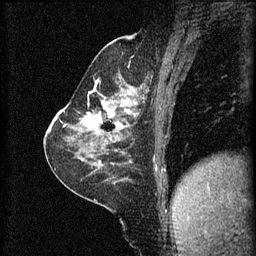
Breast MRI (dynamic contrast-enhanced), one sagittal slice. Position 30 of 60 along the scan axis. 3 images stored at this slice position (order not interpretable as contrast timing). 1.5 T. TE 4.2 ms, TR 8.2 ms. 2 mm slice thickness. 256 × 256 image matrix, field of view 180 × 180 mm. Patient: female, 59 years.
Structures marked on this image (semi-automatically segmented with operator editing):
- analysis volume of interest (the breast-tissue region the enhancement analysis was run in; not a lesion): box from (x=78, y=92) to (x=137, y=135) px
- tumour enhancement mask (voxels above the 70 % enhancement threshold inside the analysis volume of interest): (x=82, y=98)–(x=131, y=129)